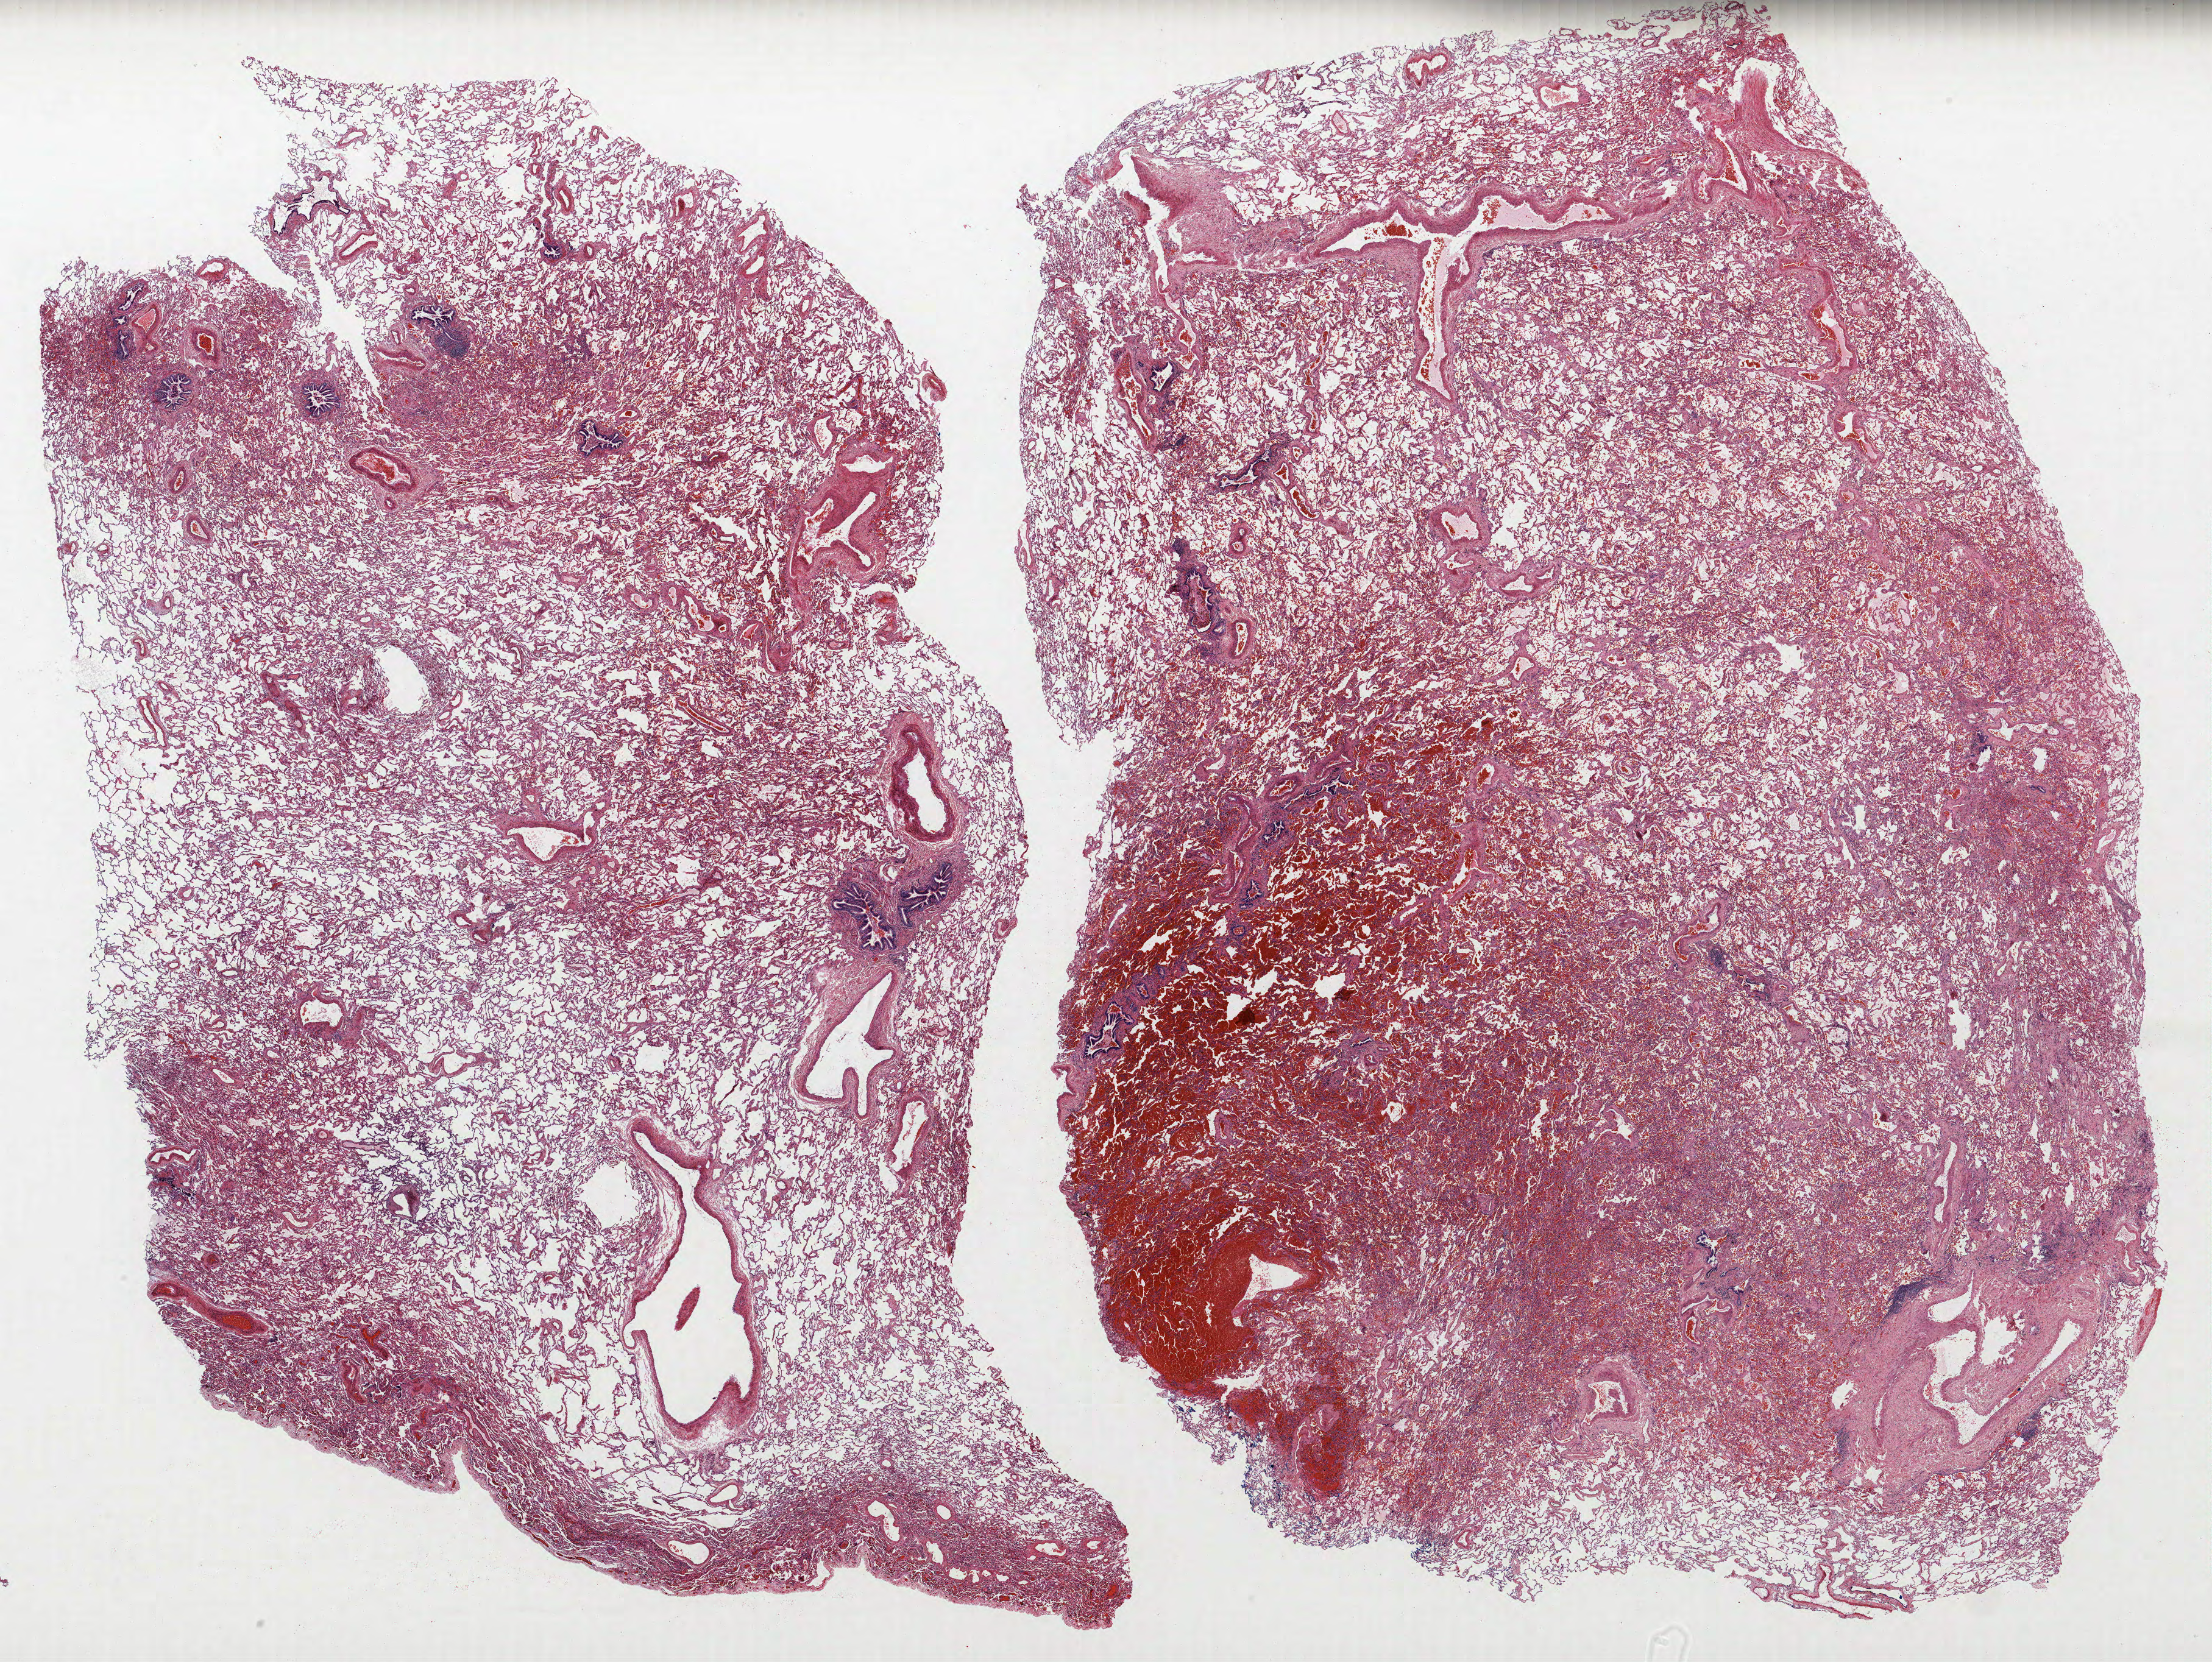
Hematoxylin and eosin (H&E) stained whole-slide image — a low-resolution overview of the entire scanned area, about 29.0 x 21.8 mm; formalin-fixed paraffin-embedded (FFPE) section; lung tissue. Male, age 56 at enrolment. Grade: poorly differentiated (G3).
Stage (AJCC 6th edition): IA. Tumour size (pathology): 24 mm. Primary tumour location (clinical record): right lower lobe. Participant's lung-cancer diagnosis: Adenocarcinoma, NOS.